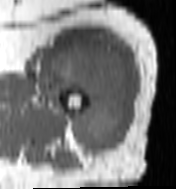
MRI of an extremity soft-tissue mass, one axial slice; slice 79 of 100 in the series (ordered by position); MR volume resampled by the dataset authors to the PET/CT grid (not the native acquisition matrix); 3.27 mm slice thickness; 176 × 189 image matrix. Female patient. Case-level facts recorded for this patient, not image findings: histological type: undifferentiated – high grade; grade: high; site of the primary tumour: left thigh.
Structures marked on this image (expert contour drawn on MRI and transferred to this co-registered scan by the dataset authors):
- gross tumour volume including surrounding oedema: box from (x=48, y=45) to (x=127, y=156) px
- gross tumour volume (mass): (x=50, y=52)–(x=125, y=152)